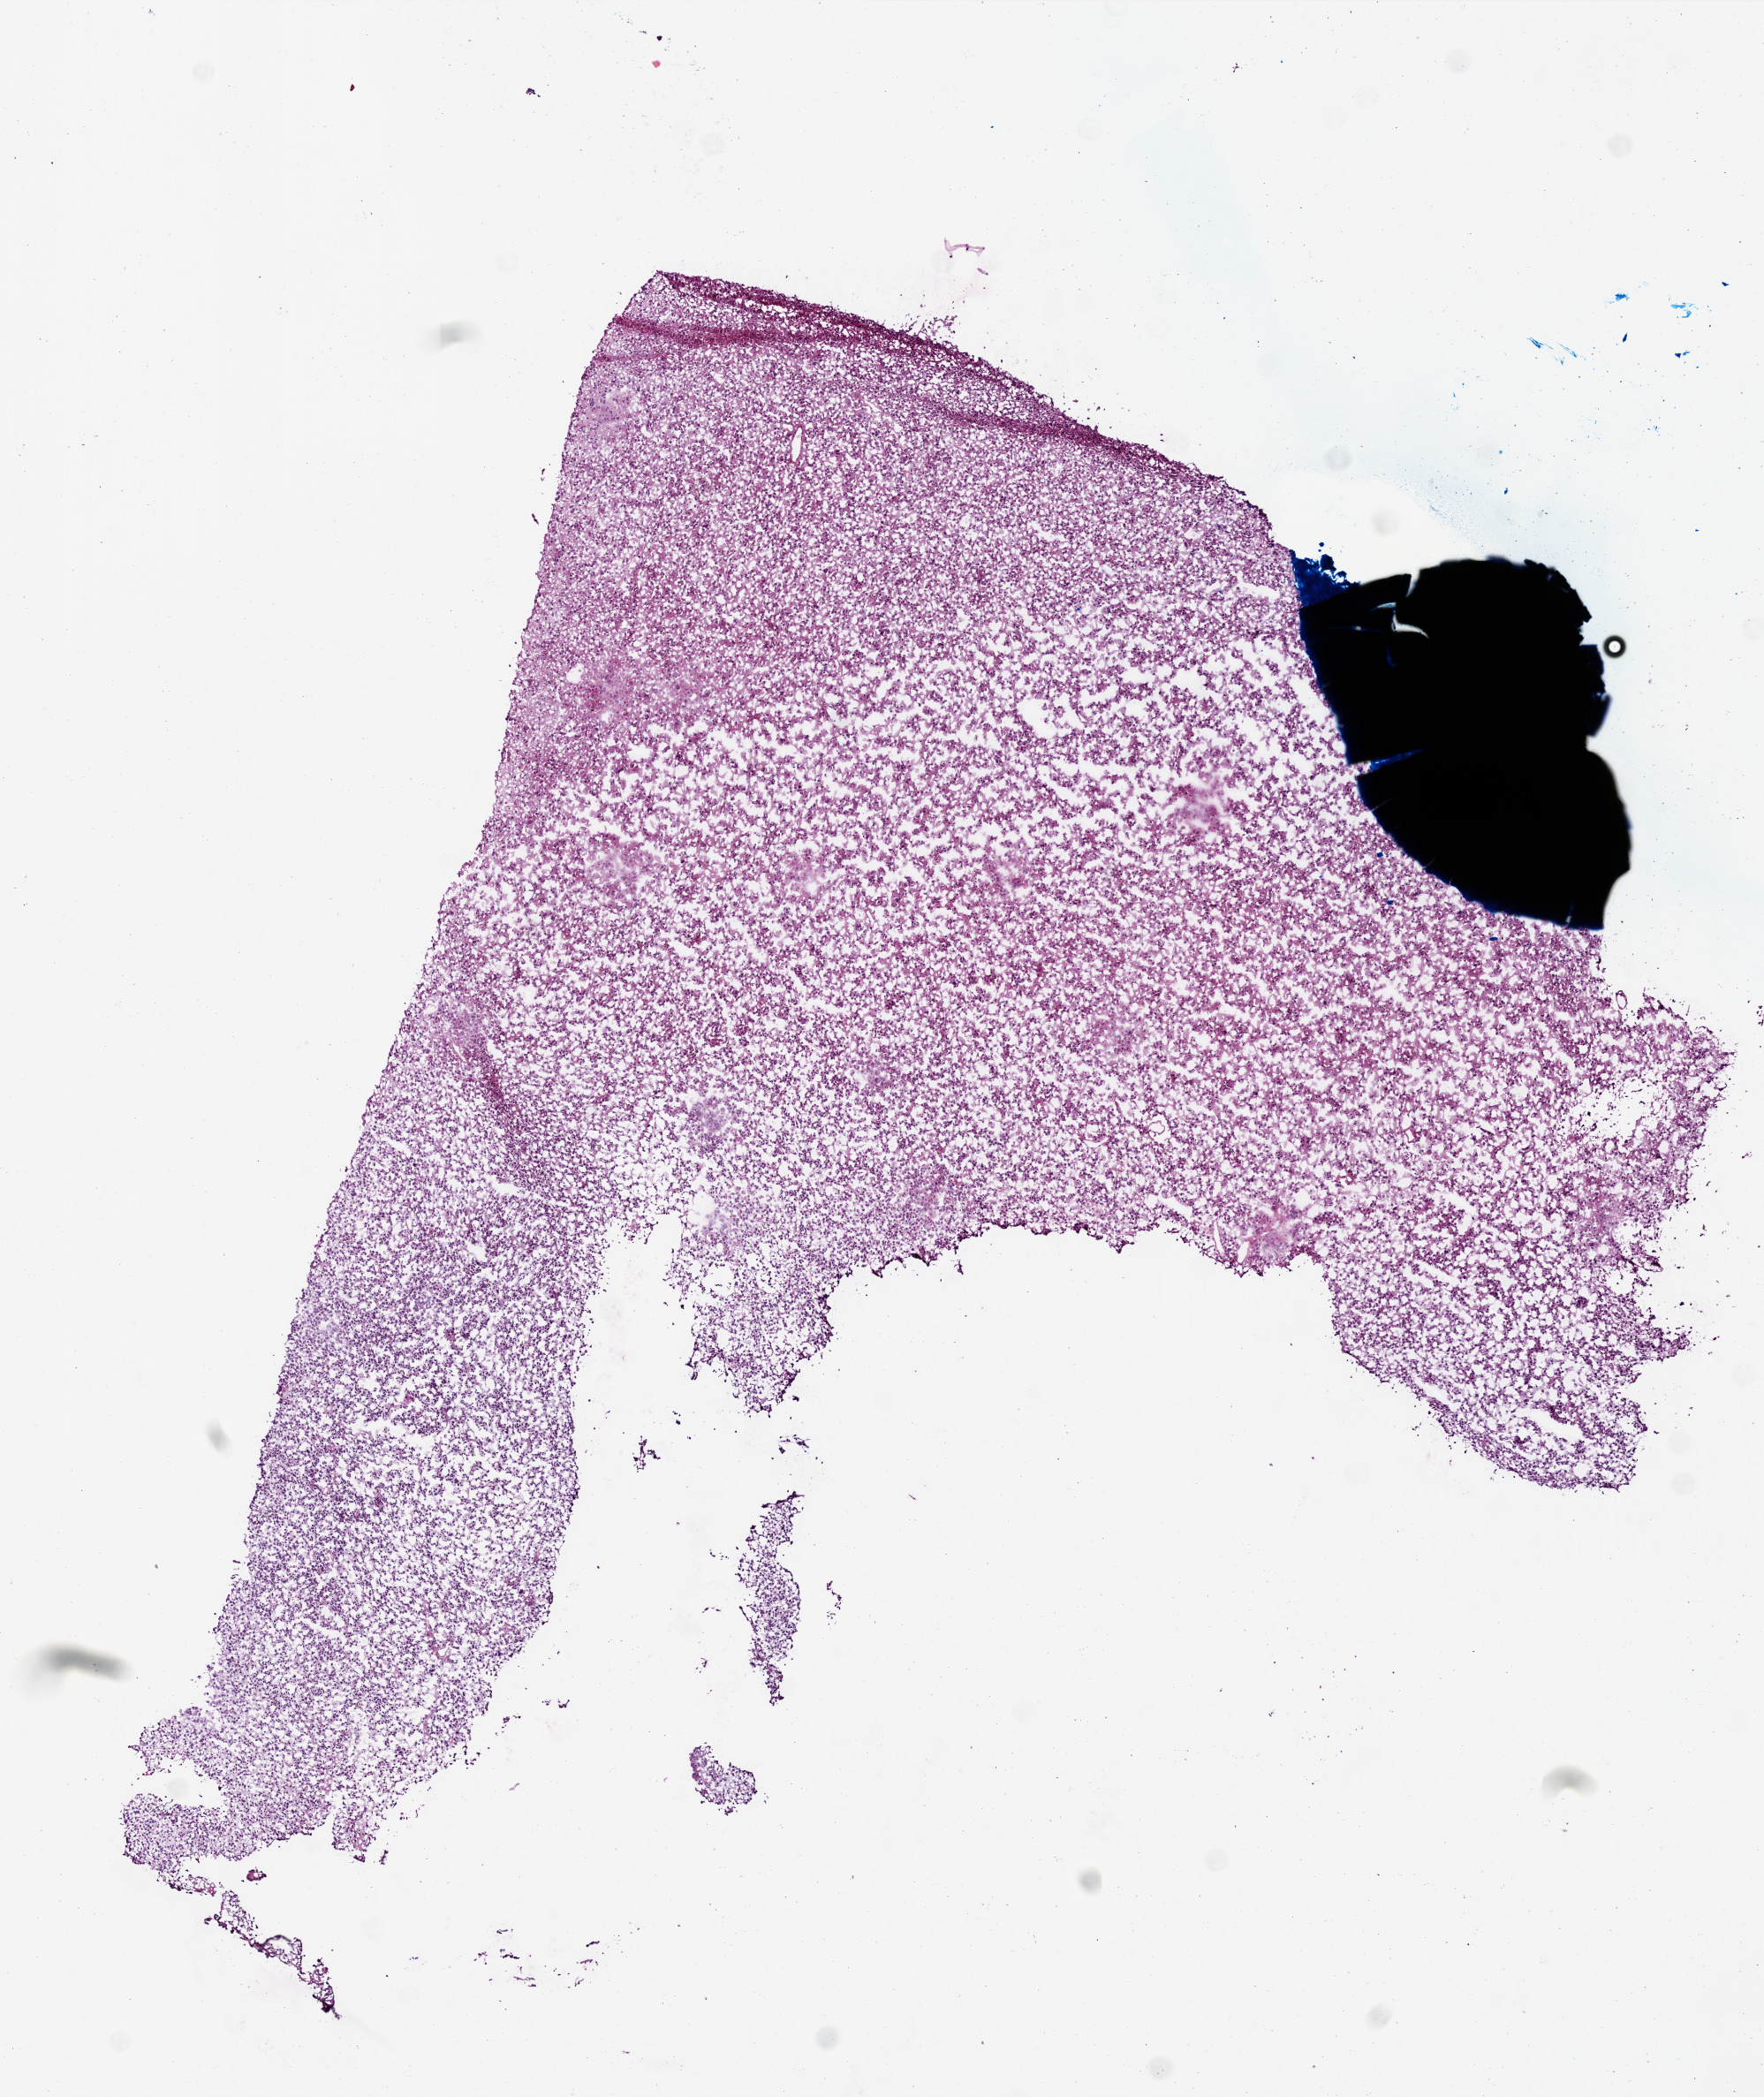
Digitized H&E tissue section (whole slide), whole scanned area (about 8.0 x 9.5 mm, acquisition: 20x scan) shown as a low-resolution overview, frozen section from the top of the tissue portion, sample: primary tumour, brain. Female patient; age at initial diagnosis 36 years. Pathologist review of this section (percent, as recorded): tumour cells 80%, tumour nuclei 90%, normal cells 0%, stromal cells 5%, necrosis 15%.
Pathologic diagnosis: Glioblastoma.